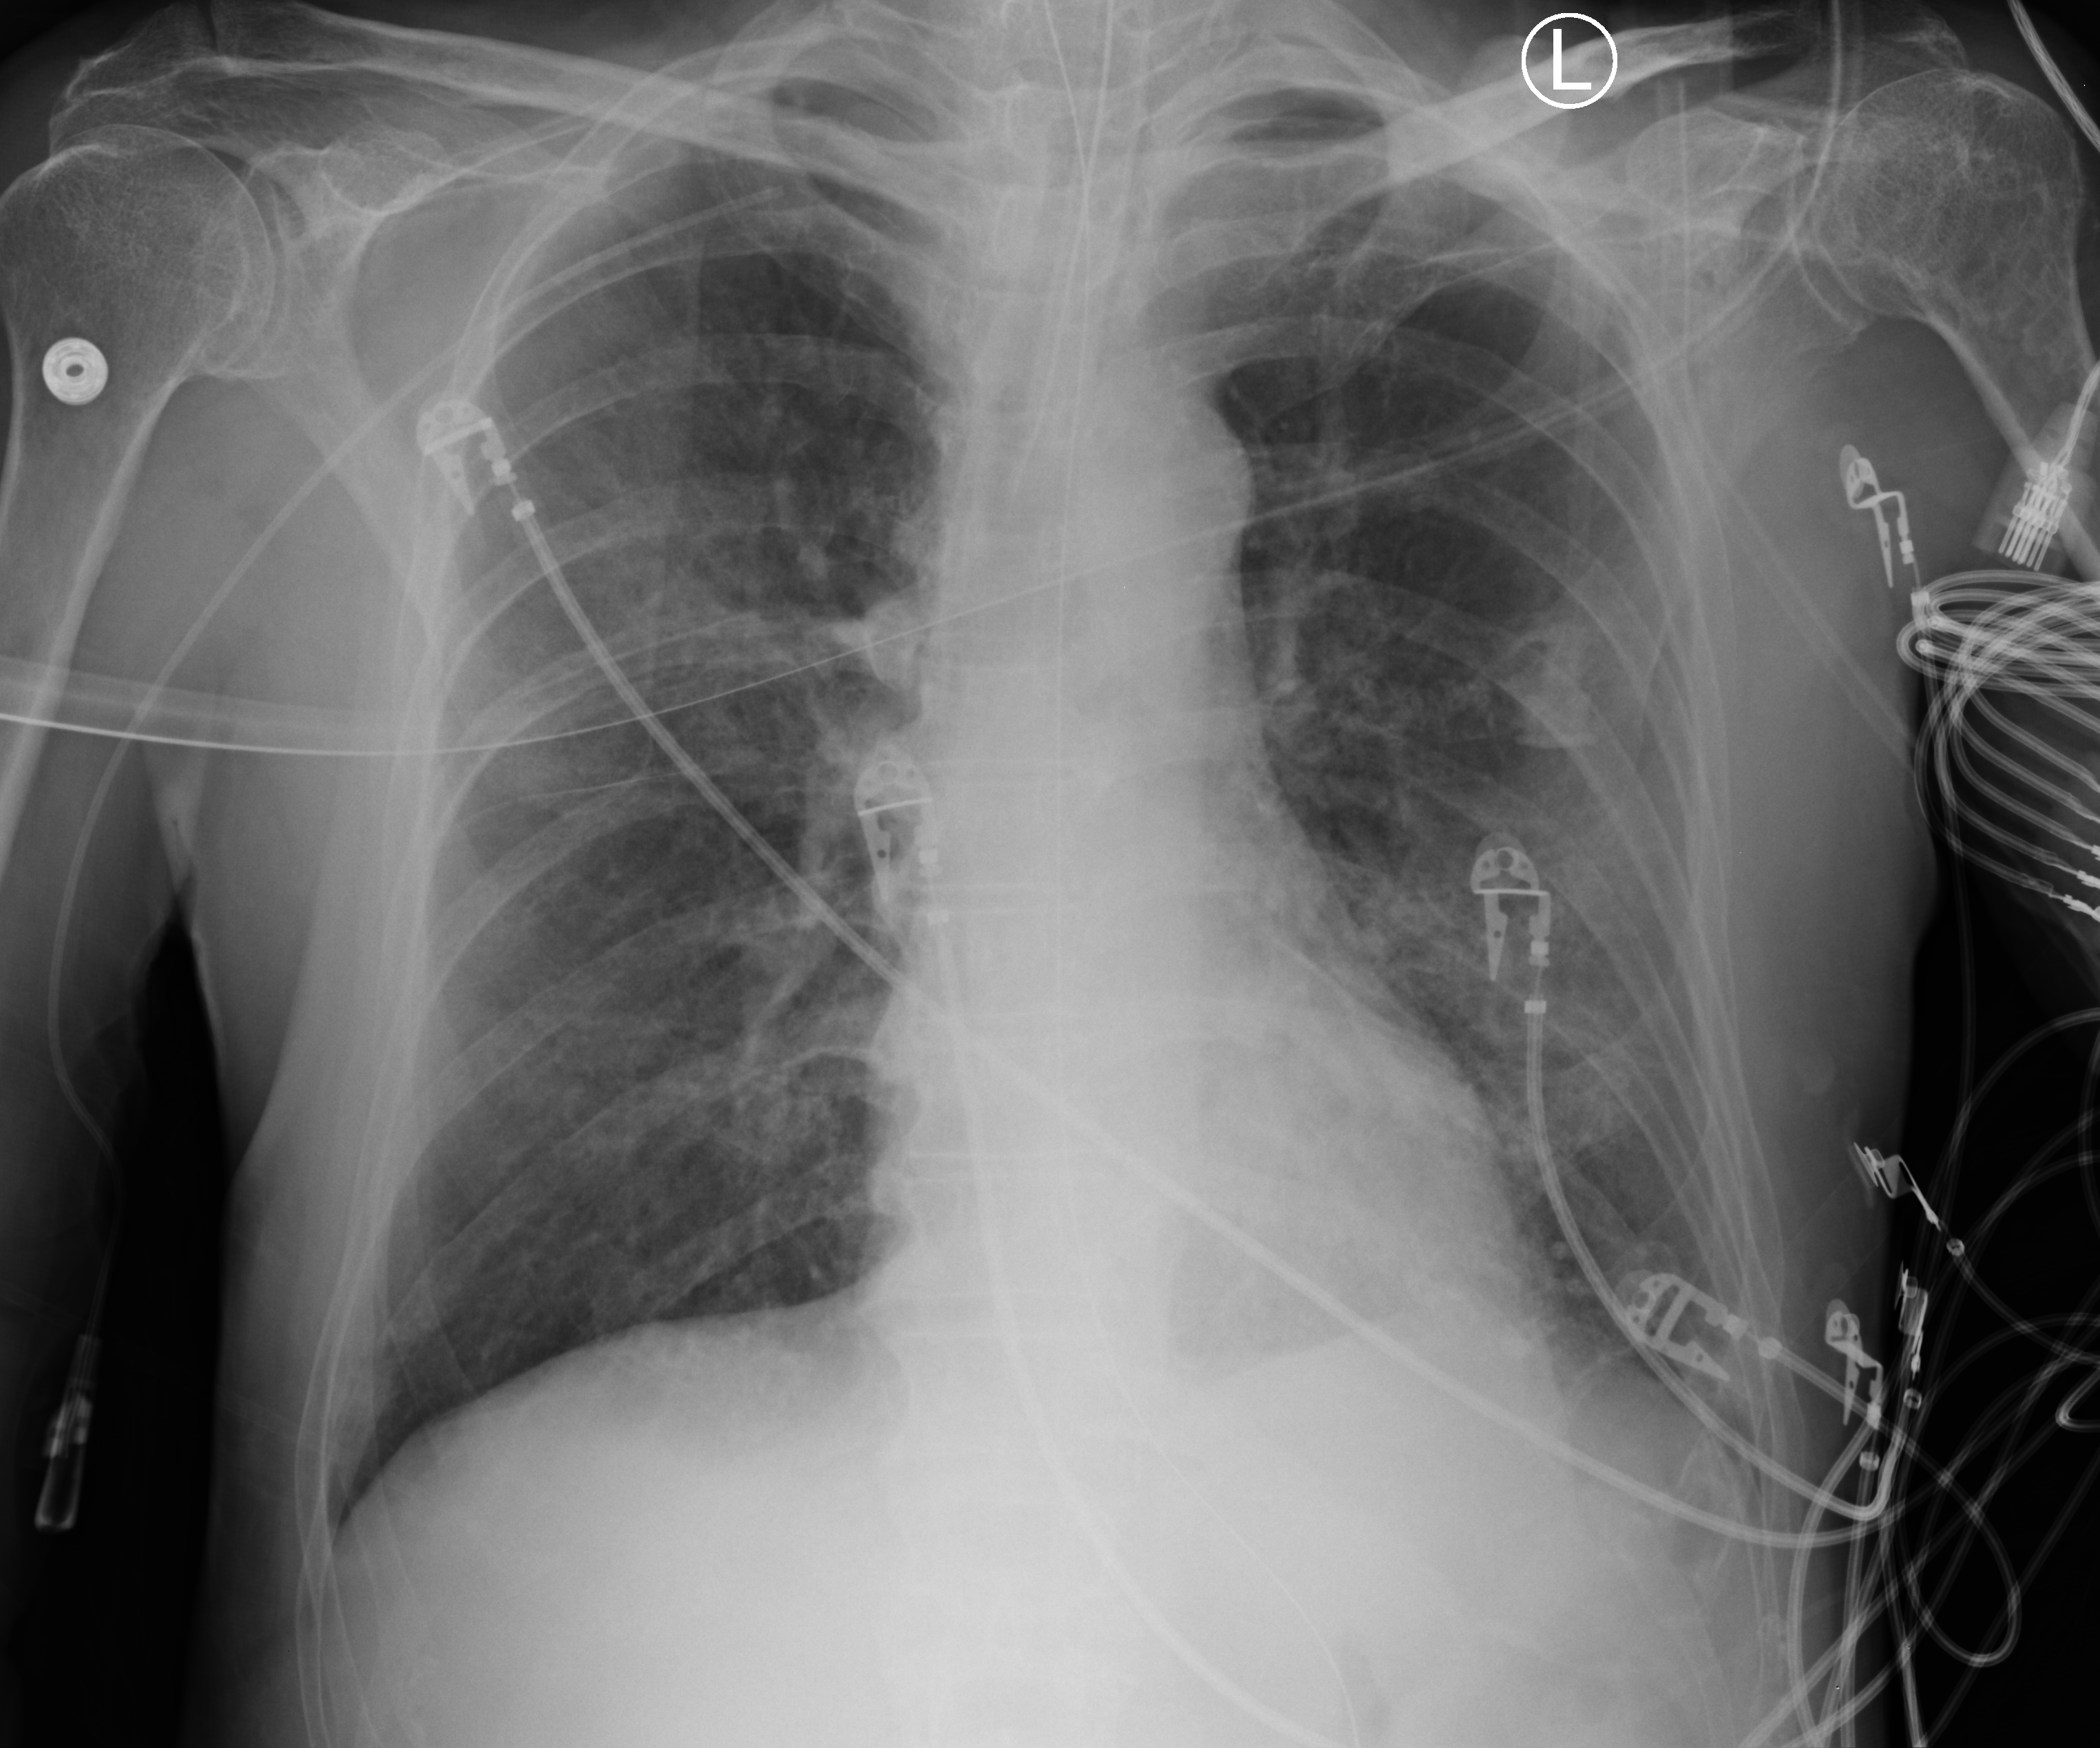
Bedside chest radiograph (computed radiography); anteroposterior (AP) projection. Patient hospitalised with COVID-19; male, aged 60–74 years.
Hospital-stay facts (about this admission, not read from this image; timing relative to this image not recorded): admitted to intensive care during this hospital stay: yes.